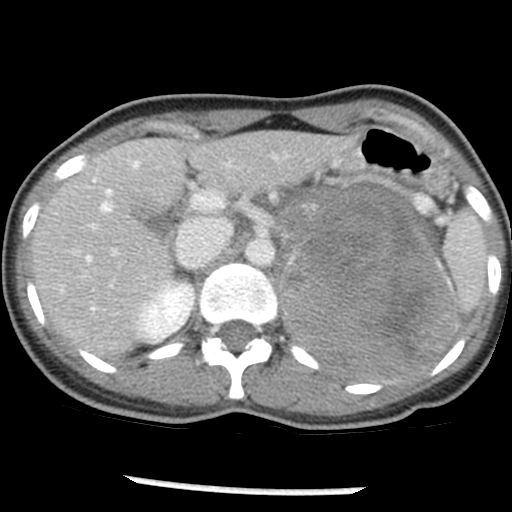
Contrast-enhanced abdominal CT, one axial slice; position 31 of 54 along the scan axis; 120 kVp; intravenous contrast given; soft-tissue window (W 400 / L 40 HU); 5 mm slice thickness; 512 × 512 image matrix, field of view 240 × 240 mm. Patient: female, 33 years. Case-level facts recorded for this patient, not image findings: diagnosis: adrenocortical carcinoma; tumour side: left adrenal; tumour size at pathology: 11 cm; Ki-67 index: 20 %; stage (as recorded): 2.
Annotated regions visible in this slice (semi-automatically segmented with operator editing):
- mass: bounding box <273,184,459,376> (left, top, right, bottom; pixels)